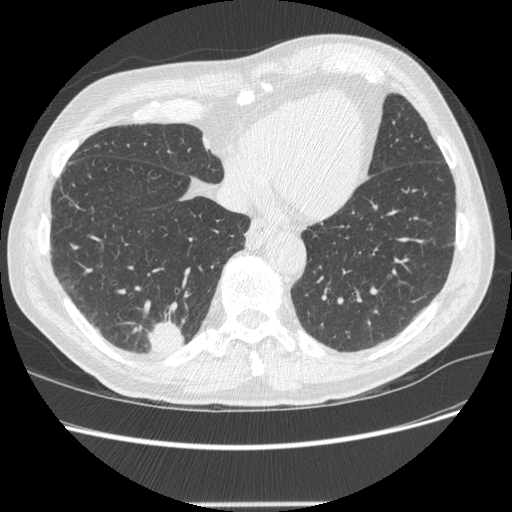
Low-dose screening chest CT, one axial slice. Slice 67 of 245 in the series (ordered by position). Reconstruction kernel STANDARD. 120 kVp. Lung window (W 1500 / L -600 HU). 1.25 mm slice thickness. 512 × 512 image matrix, field of view 372 × 372 mm.
Outlined on this slice (outlined manually by an expert reader):
- lesion 1 (tumor, lower lobe of right lung): box from (x=148, y=321) to (x=184, y=354) px